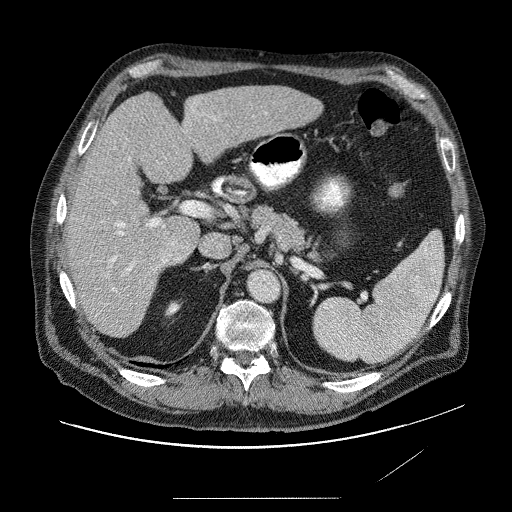
Contrast-enhanced abdominal CT (liver protocol), one axial slice. Slice 44 of 89 in the series (ordered by position). Reconstruction kernel STANDARD. 120 kVp. Soft-tissue window (W 400 / L 40 HU). 2.5 mm slice thickness. 512 × 512 image matrix, field of view 420 × 420 mm. Case-level facts recorded for this patient, not image findings: diagnosis: hepatocellular carcinoma (patient treated with transarterial chemoembolisation; whether this scan precedes or follows treatment is not stated here); TNM stage (as recorded): Stage-IVA; Child-Pugh class: A; tumour differentiation: moderately differentiated.
Annotated regions visible in this slice (semi-automatically segmented with operator editing):
- liver parenchyma outside the tumour (the mass and vessels are separate outlines, so this box may not span the whole liver): bounding box <62,84,326,336> (left, top, right, bottom; pixels)
- mass: <151,155,197,264>
- liver vessels: <105,113,270,292>